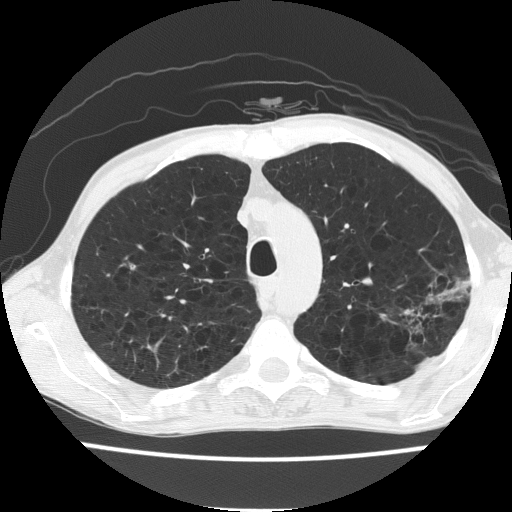
Low-dose screening chest CT, axial slice; first (baseline) screen; lung window (W 1500 / L -600 HU); 2 mm slice thickness; 512 × 512 image matrix, field of view 320 × 320 mm. Male, age 60 years at enrolment. Current smoker at enrolment.
- Lesion marked by an expert reader, box from (x=391, y=255) to (x=475, y=343) px.
- No non-calcified nodule or mass ≥4 mm was recorded by the screening reader at this exam.
- Later outcome: lung cancer diagnosed 490 days after this screen (after the second annual screen) — bronchiolo-alveolar carcinoma, mucinous, left upper lobe, stage IV (AJCC 6th edition).